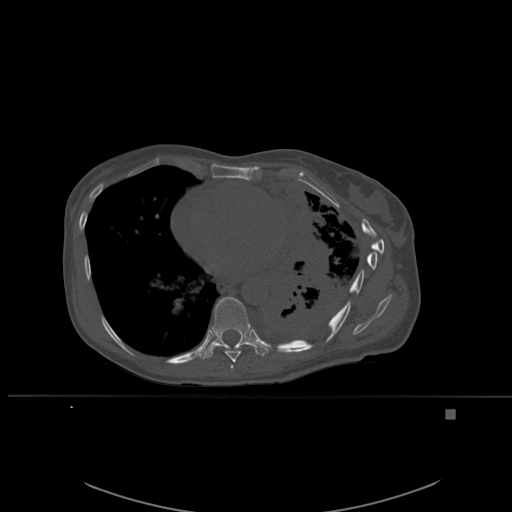
CT including the spine, one axial slice; slice 341 of 537 in the series (ordered by position); bone window (W 1800 / L 400 HU); 1.5 mm slice thickness; 512 × 512 image matrix. Female patient, age 45 years. From the clinical record (not read from this slice): primary cancer: lung.
Annotated regions visible in this slice (semi-automatically segmented with operator editing):
- T7 vertebra: box from (x=230, y=365) to (x=234, y=369) px
- T8 vertebra: (x=214, y=344)–(x=248, y=362)
- T9 vertebra: (x=200, y=297)–(x=269, y=360)